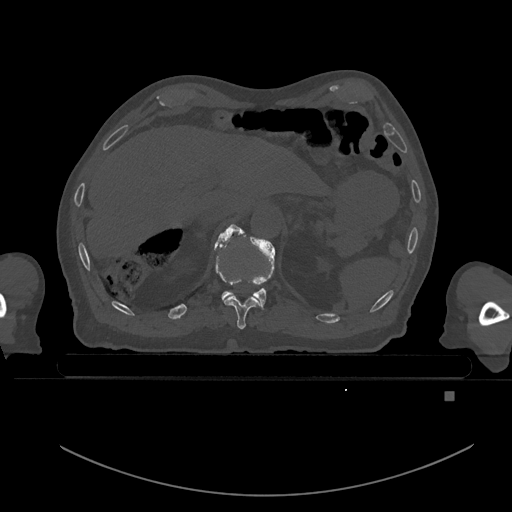
CT including the spine, one axial slice. Slice 62 of 969 in the series (ordered by position). Bone window (W 1800 / L 400 HU). 0.5 mm slice thickness. 512 × 512 image matrix, field of view 456 × 456 mm. Male patient, age 82 years. From the clinical record (not read from this slice): primary cancer: prostate.
Annotated regions visible in this slice (semi-automatically segmented with operator editing):
- T10 vertebra: box from (x=214, y=240) to (x=261, y=330) px
- T11 vertebra: (x=218, y=224)–(x=276, y=307)